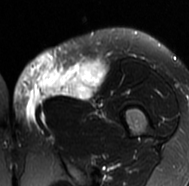
MRI of an extremity soft-tissue mass, one axial slice; position 28 of 77 along the scan axis; T2-weighted fat-saturated; MR volume resampled by the dataset authors to the PET/CT grid (not the native acquisition matrix); 189 × 186 image matrix. Female patient. Case-level facts recorded for this patient, not image findings: histological type: leiomyosarcoma; grade: high; site of the primary tumour: groin.
Outlined on this slice (expert contour drawn on MRI and transferred to this co-registered scan by the dataset authors):
- gross tumour volume including surrounding oedema: bounding box <13,52,105,130> (left, top, right, bottom; pixels)
- gross tumour volume (mass): <42,61,103,99>